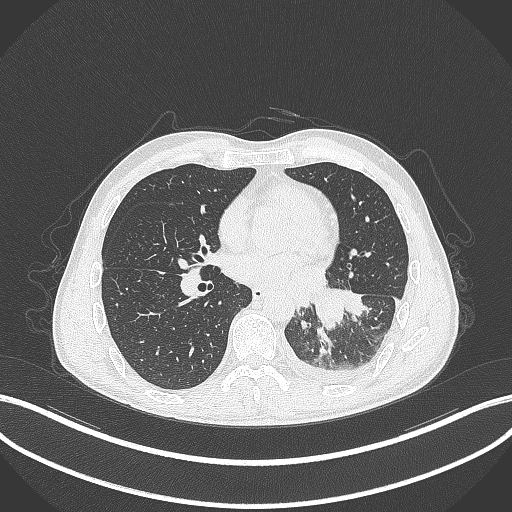
Chest CT, one axial slice. Position 138 of 295 along the scan axis. 120 kVp. Lung window (W 1500 / L -600 HU). 1 mm slice thickness. 512 × 512 image matrix, field of view 400 × 400 mm. Patient: male, 47 years. From the clinical record (not read from this slice): clinical TNM (as recorded): T3 N1 M1c.
Annotated regions visible in this slice (bounding box drawn by a radiologist):
- lung tumour (recorded histology: small cell carcinoma): bounding box (x1, y1, x2, y2) in pixels: (313, 286, 346, 331)